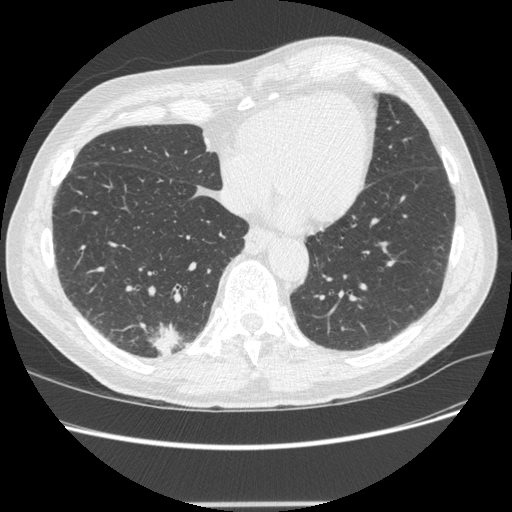
Low-dose screening chest CT, one axial slice. Slice 73 of 245 in the series (ordered by position). 120 kVp. Lung window (W 1500 / L -600 HU). 1.25 mm slice thickness. 512 × 512 image matrix, field of view 372 × 372 mm.
Structures marked on this image (expert manual segmentation):
- lesion 1 (tumor, lower lobe of right lung): bounding box [x1, y1, x2, y2] px = [150, 324, 181, 356]